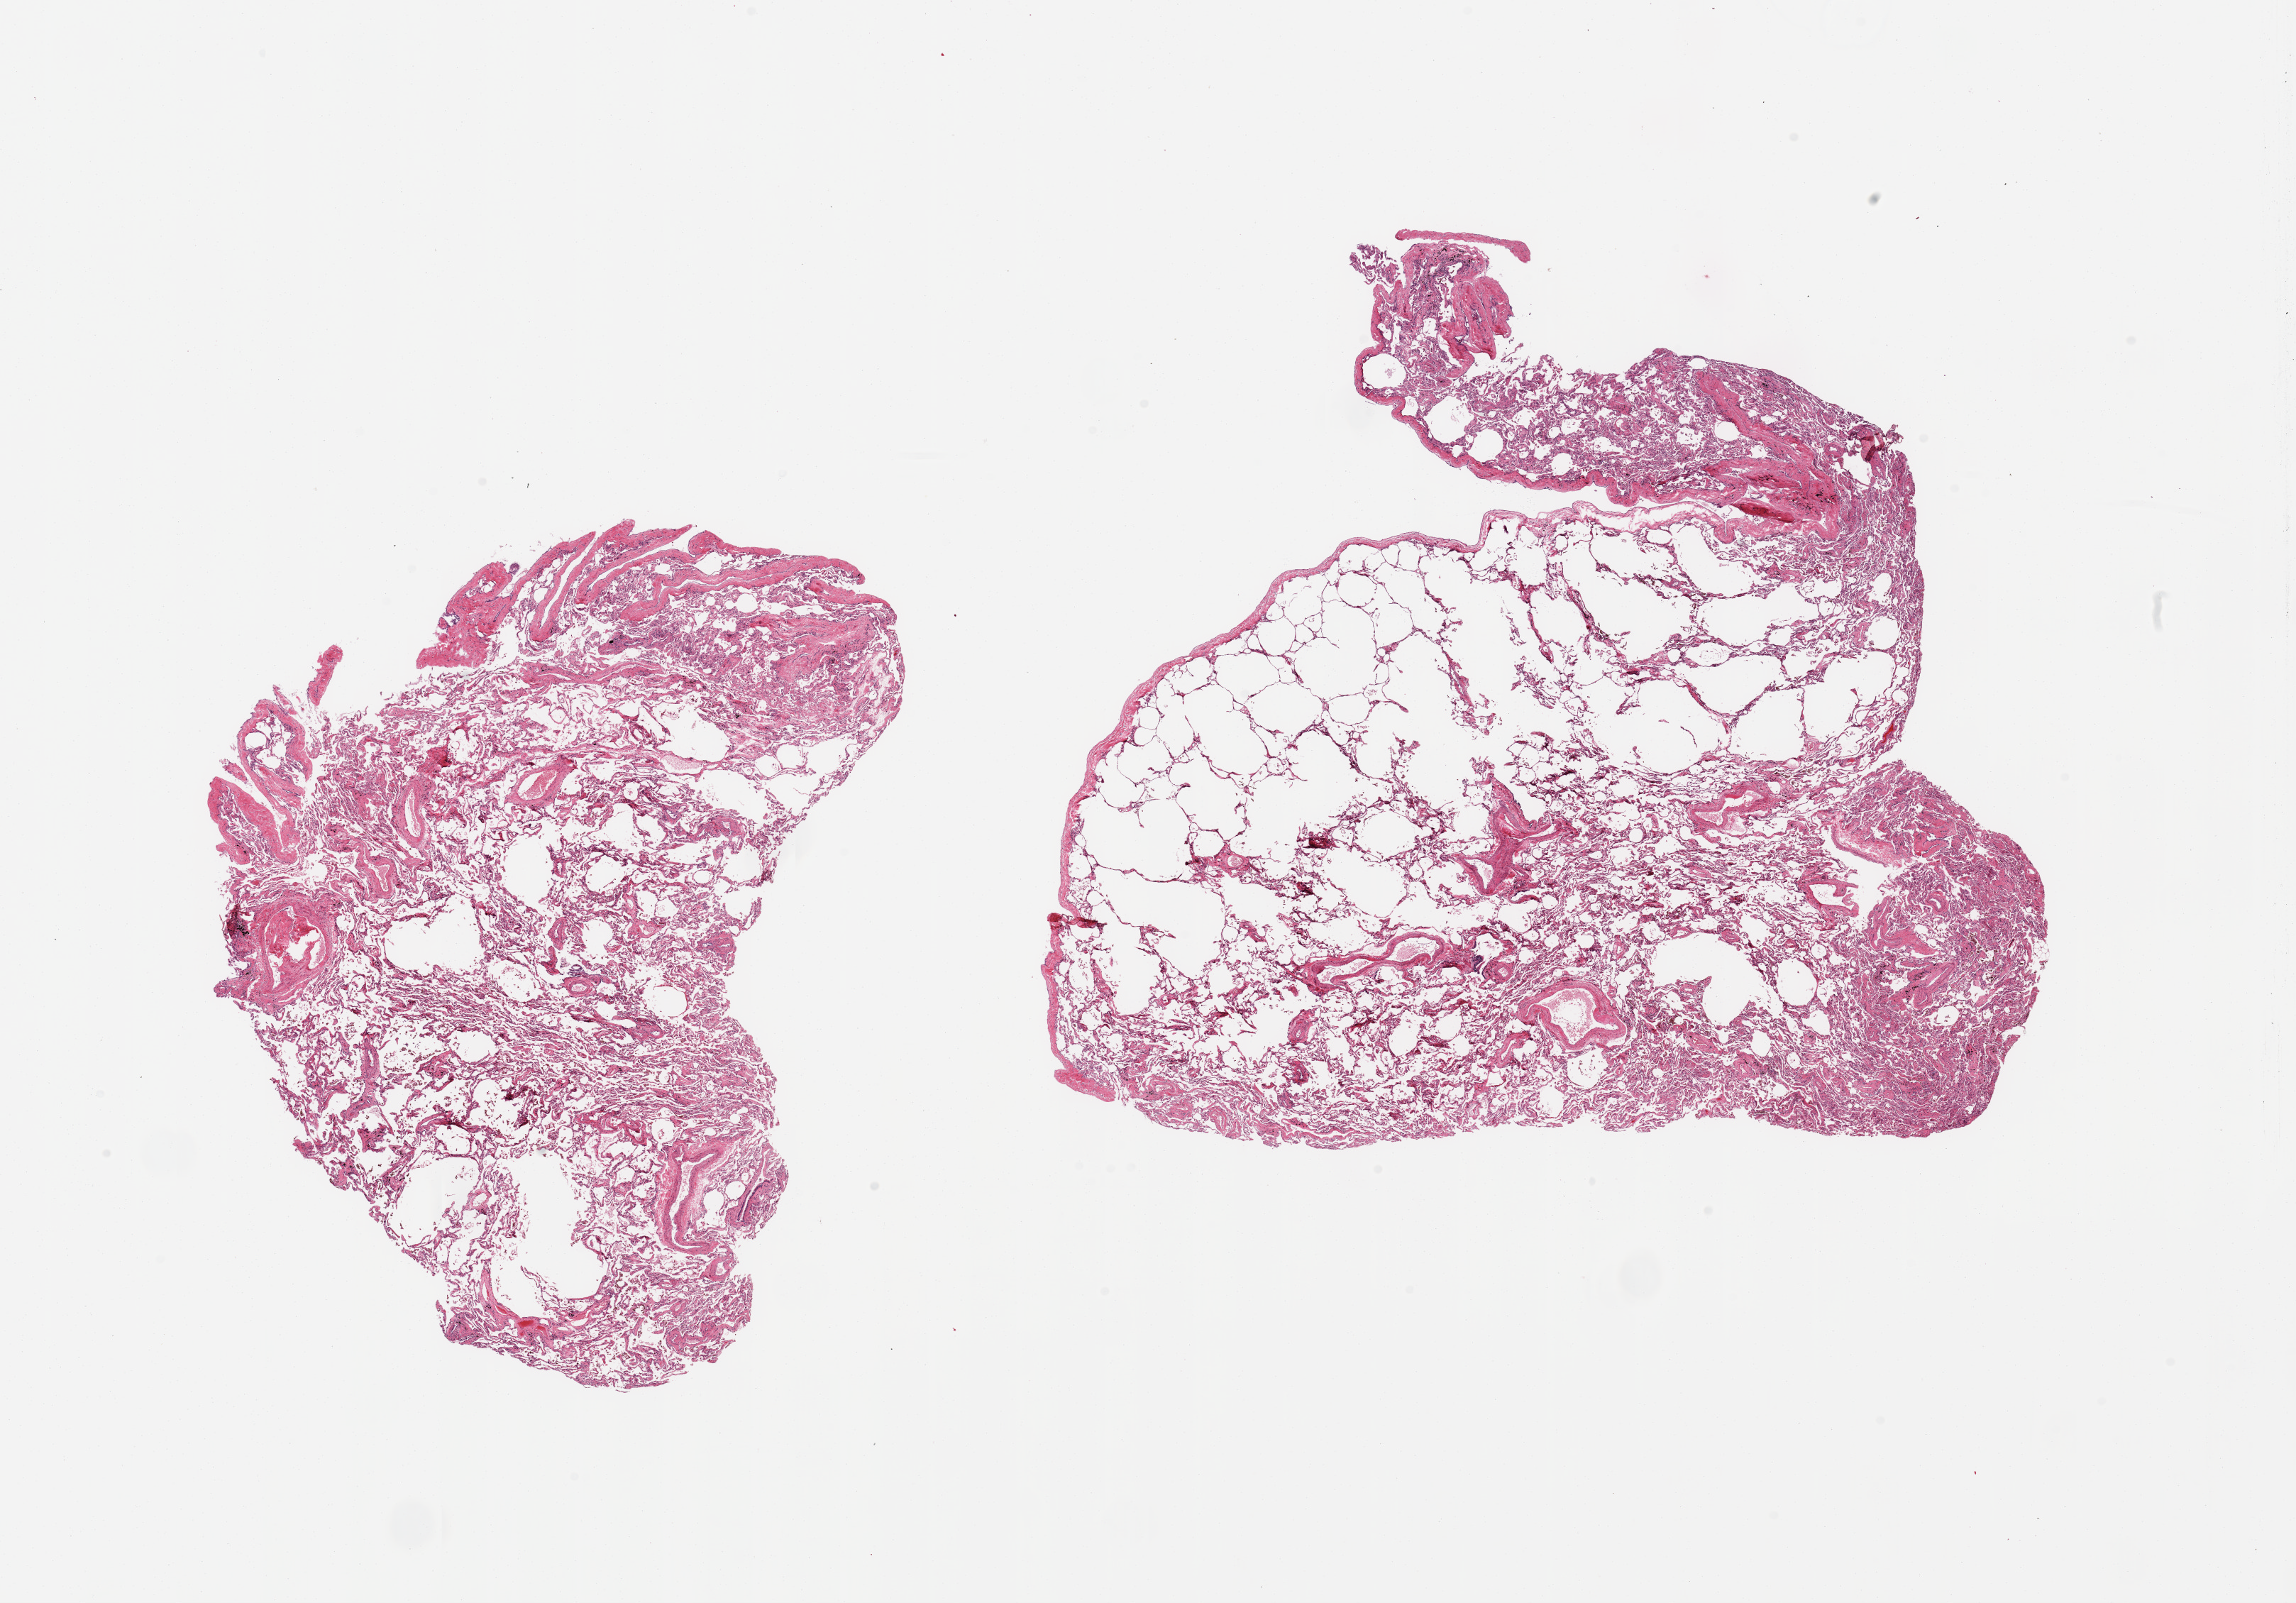
Hematoxylin and eosin (H&E) whole-slide image, whole scanned area (about 25.6 x 17.9 mm, slide scanned at 20x) shown as a low-resolution overview. PAXgene-fixed paraffin-embedded (PFPE) section. Target tissue: lung. Tissue donor sample.
Pathologist's review note for this sample: 2 pieces; small numbers of pigmented alveolar macrophages; hyperaerated area, no fibrosis.